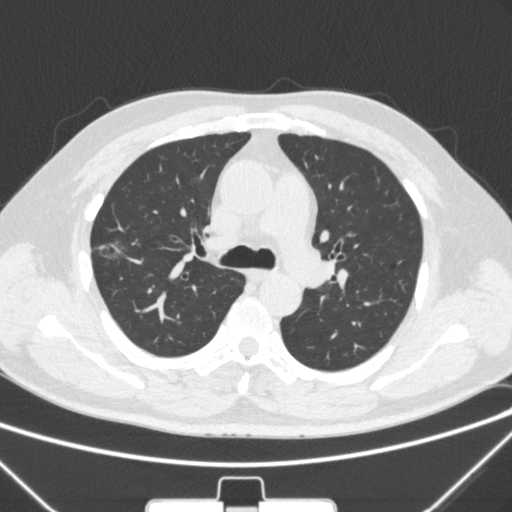
Chest CT, one axial slice; slice 202 of 320 in the series (ordered by position); lung window (W 1500 / L -600 HU); 1 mm slice thickness; 512 × 512 image matrix. Male patient, age 58 years. From the clinical record (not read from this slice): clinical TNM (as recorded): T1c N0 M0.
Annotated regions visible in this slice (bounding box drawn by a radiologist):
- lung tumour (recorded histology: adenocarcinoma): bounding box (x1, y1, x2, y2) in pixels: (91, 228, 130, 273)